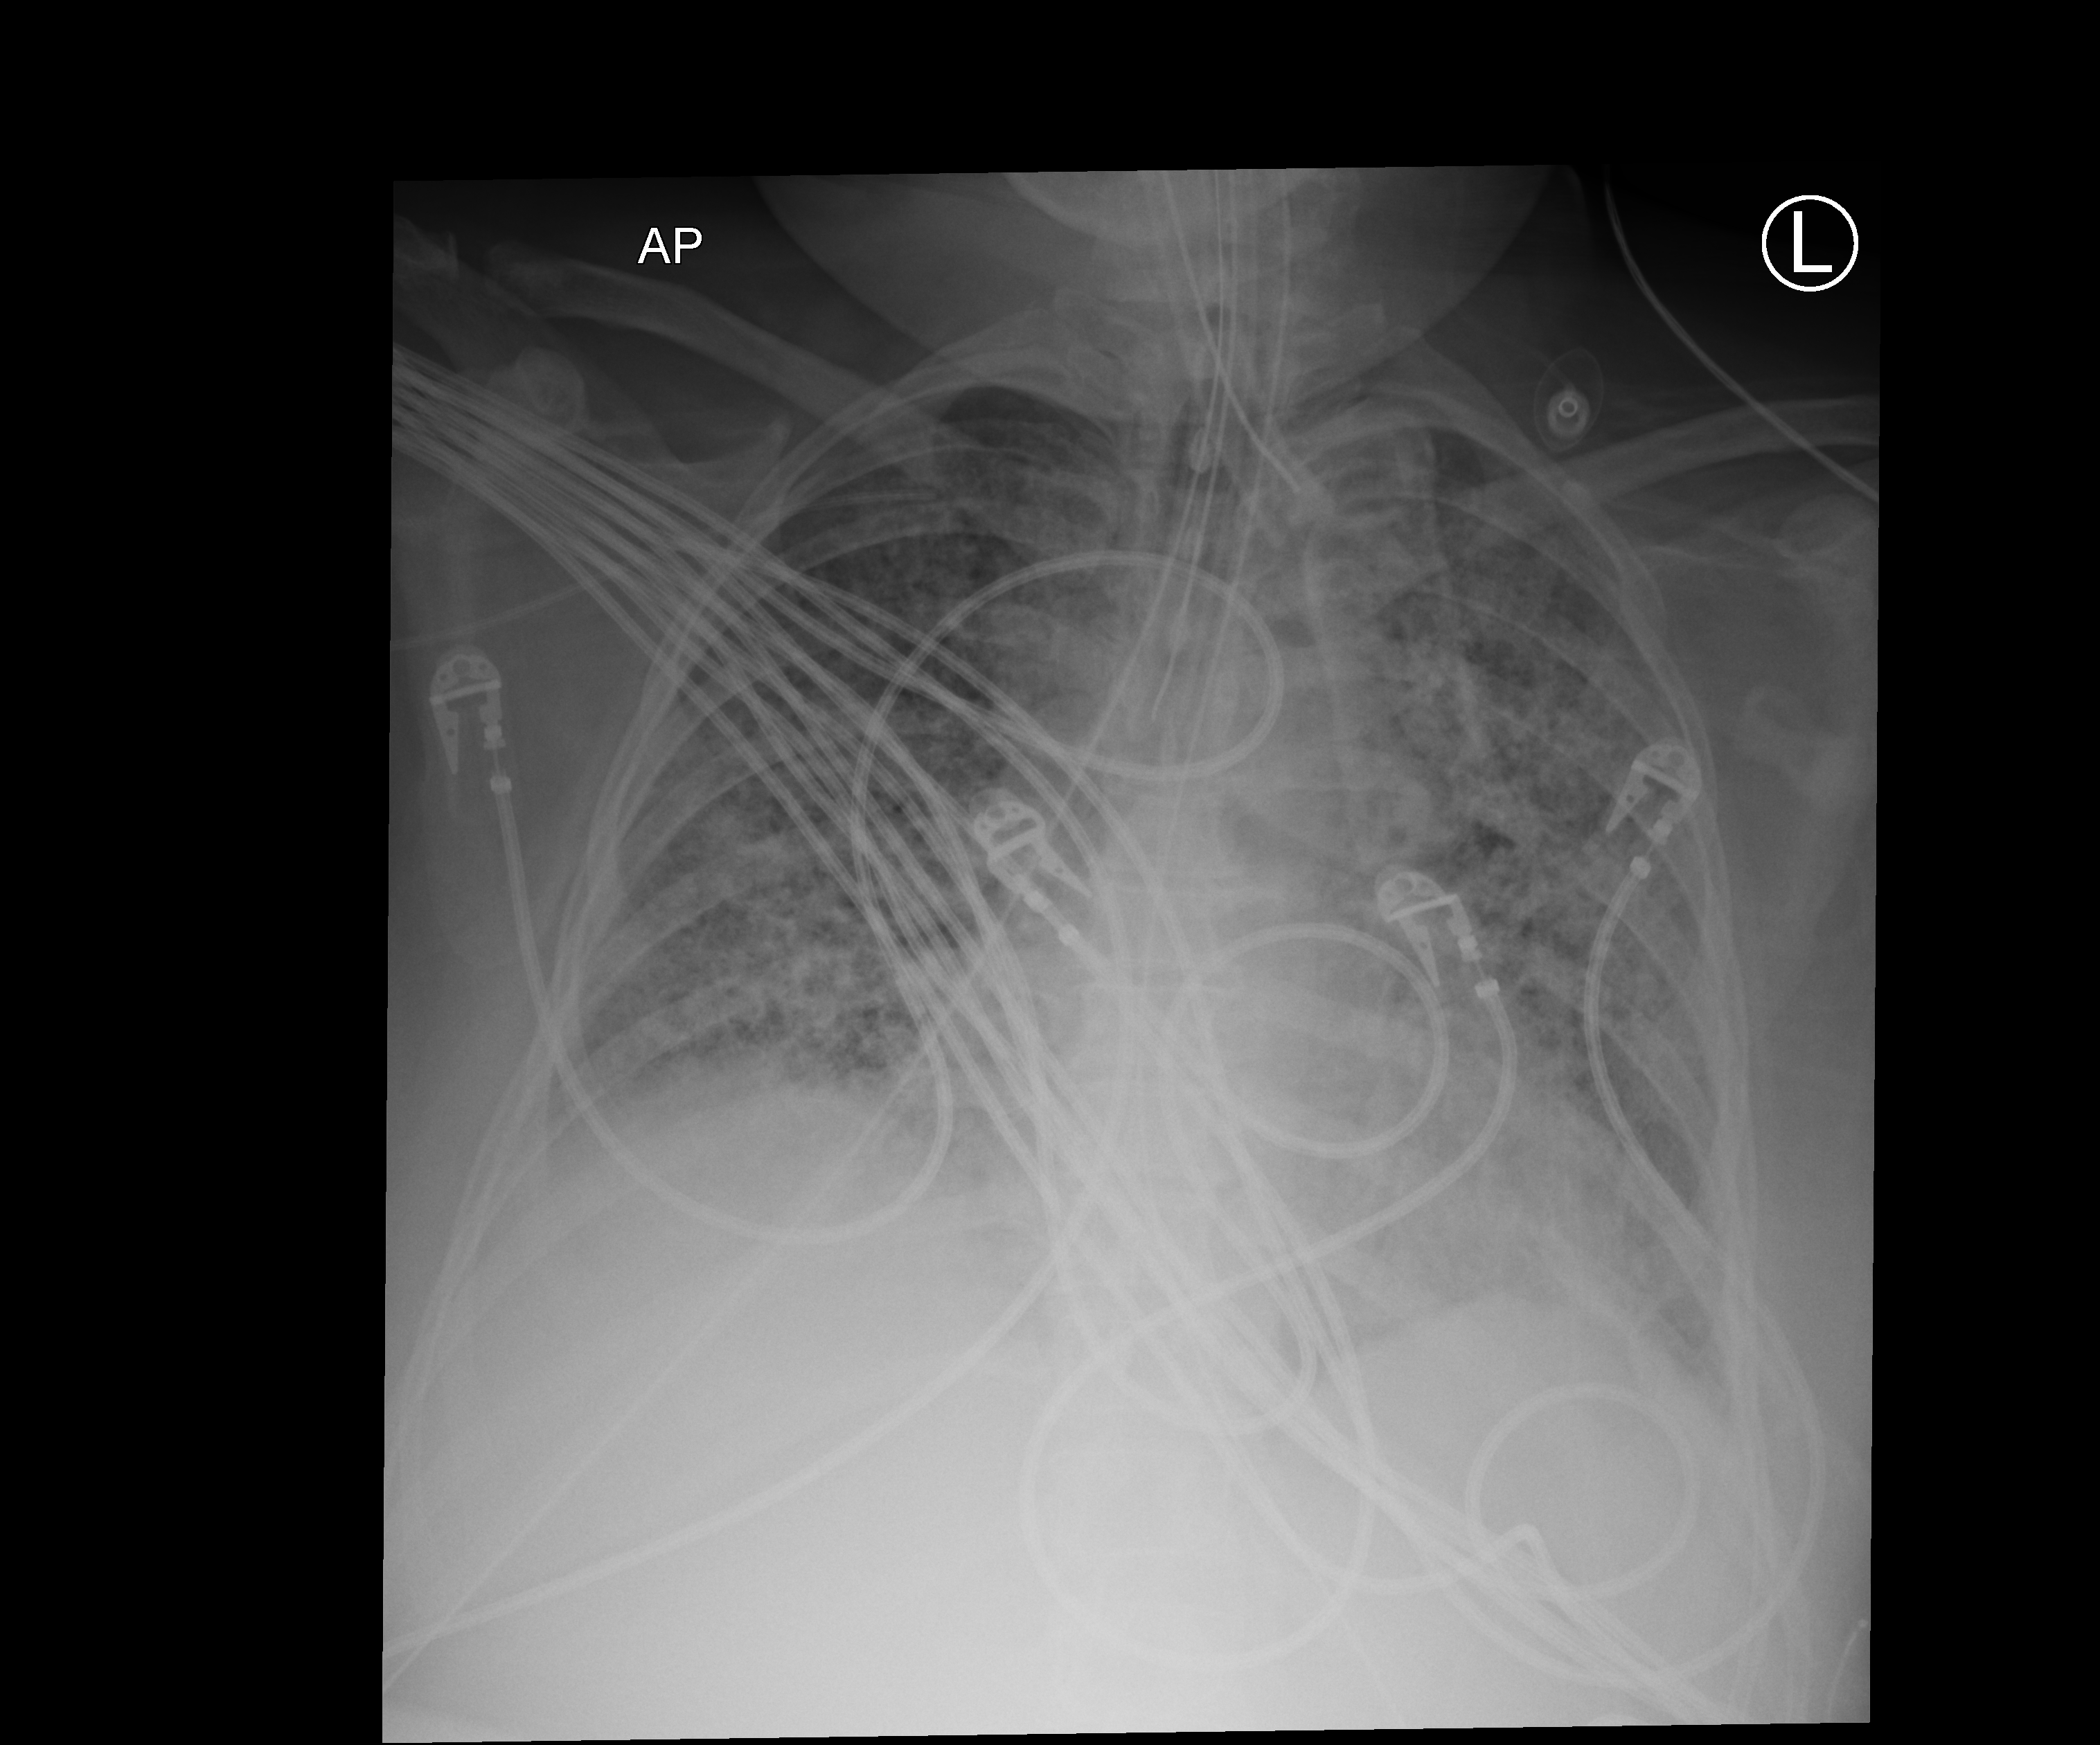
Portable chest radiograph; anteroposterior (AP) projection. Patient hospitalised with COVID-19; female, aged 18–59 years.
Hospital-stay facts (about this admission, not read from this image; timing relative to this image not recorded): admitted to intensive care during this hospital stay: yes.